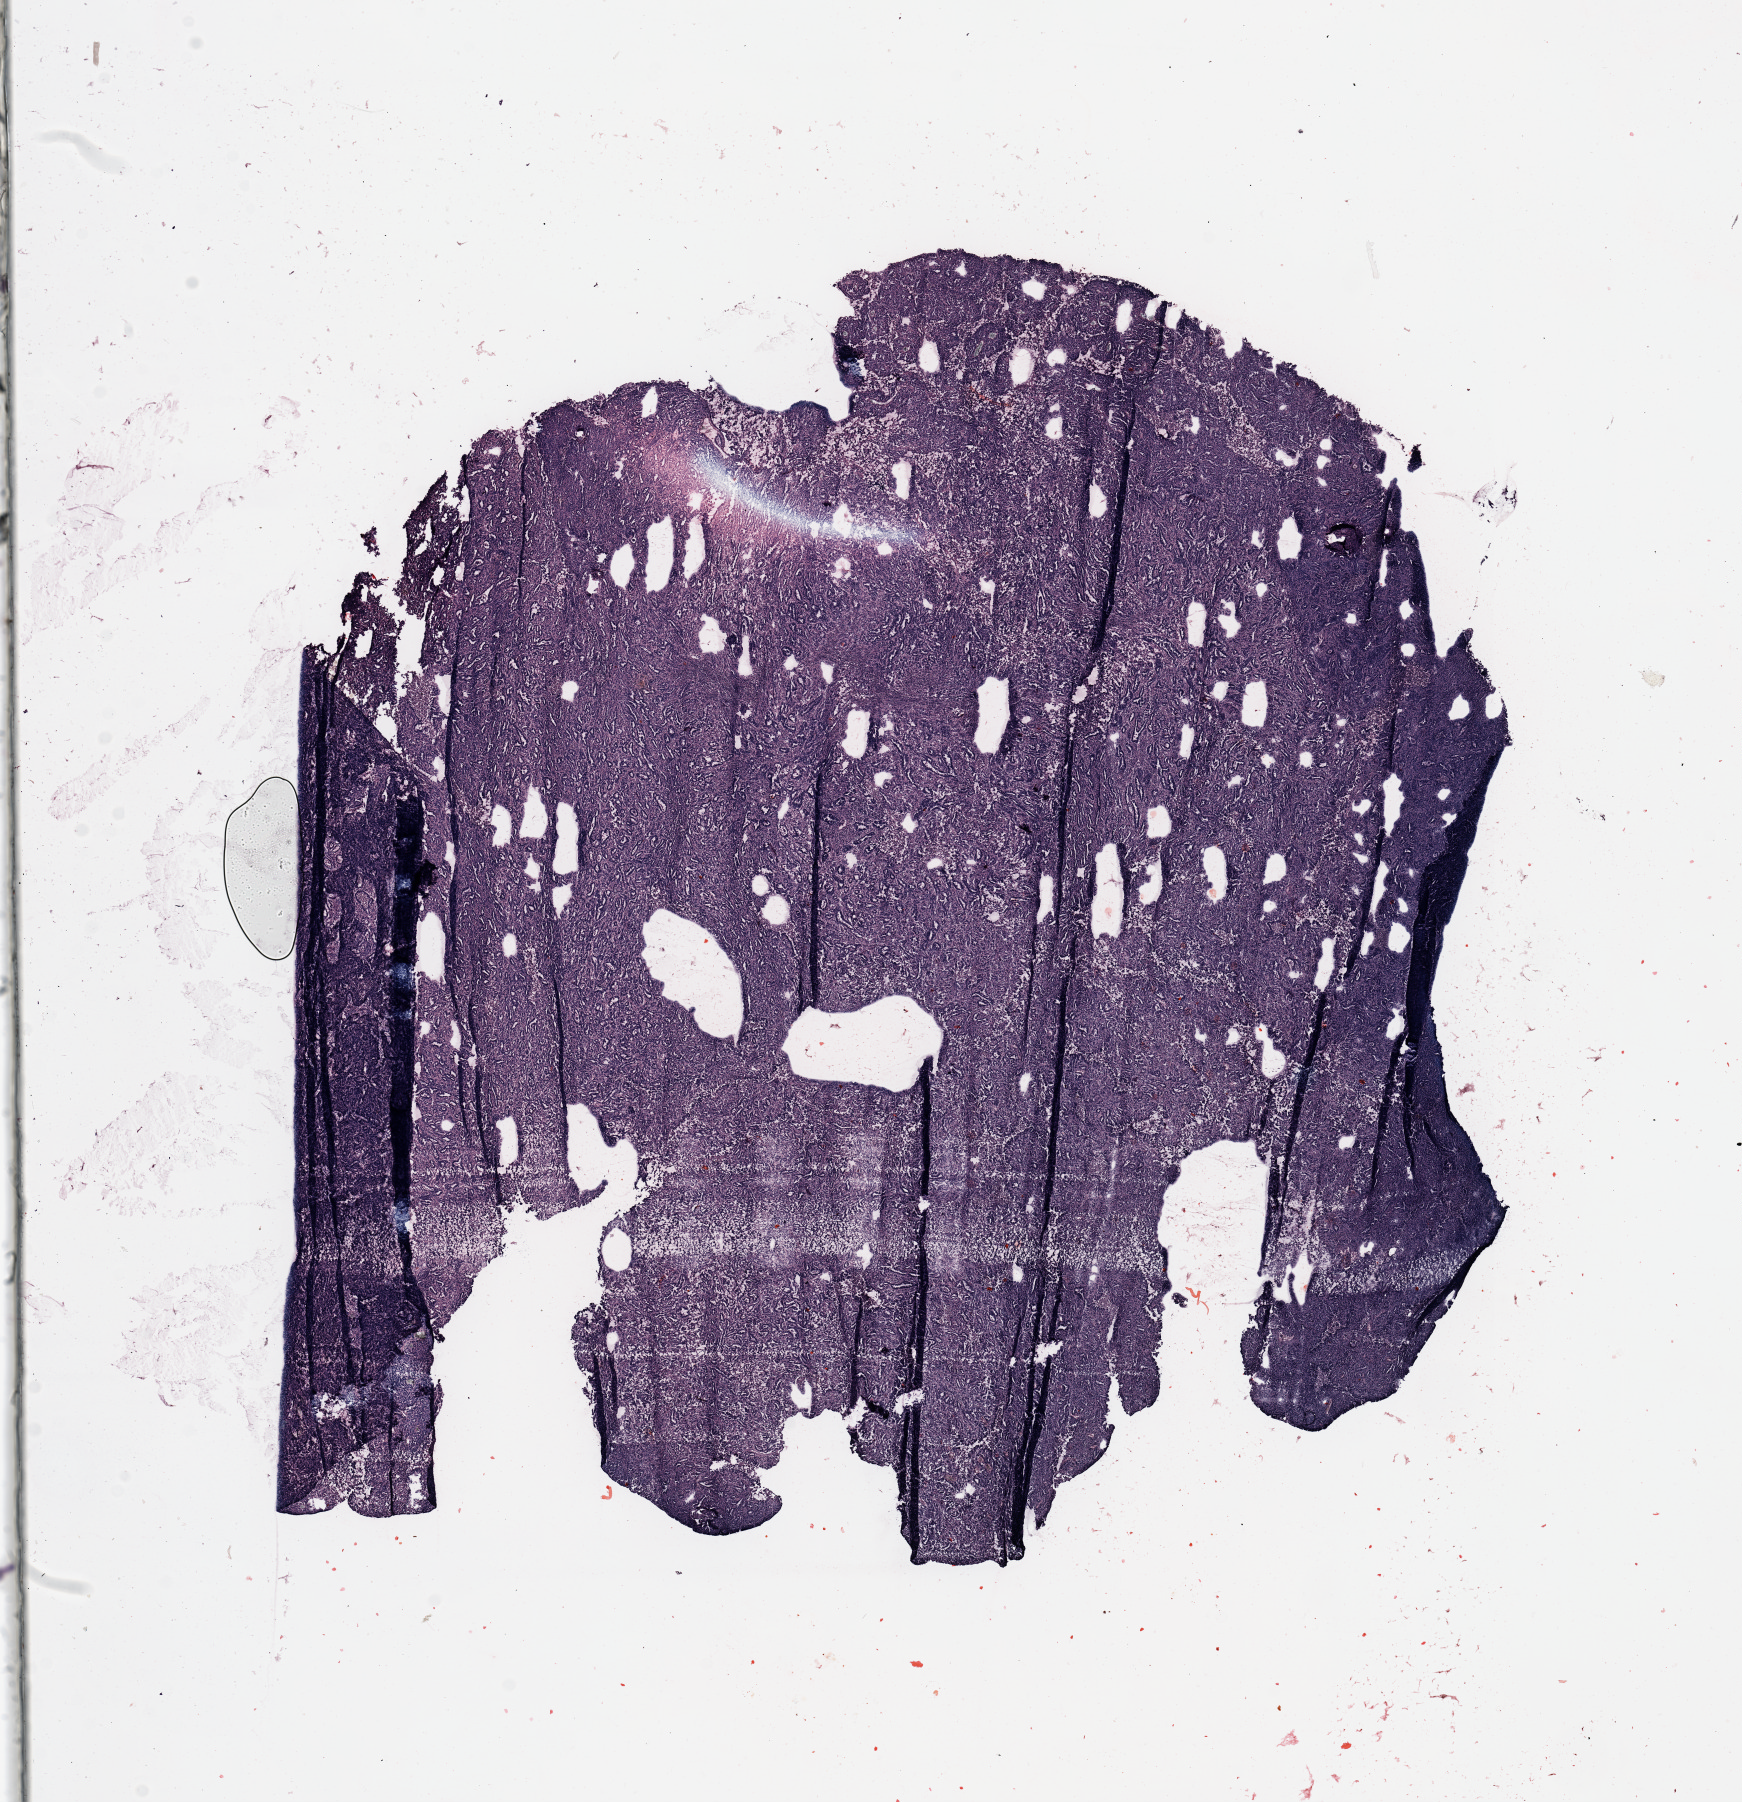
Whole-slide histology image, H&E-stained, whole scanned area (about 13.8 x 14.3 mm, slide scanned at 20x) shown as a low-resolution overview, tumour tissue sample, sampled site: uterus. Patient: female, age 60 years. Histologic grade: G3 (poorly differentiated). Slide review estimates, as recorded: tumour nuclei 90%, necrosis 0%.
- AJCC pathologic stage: III
- diagnosis: Endometrioid adenocarcinoma, NOS